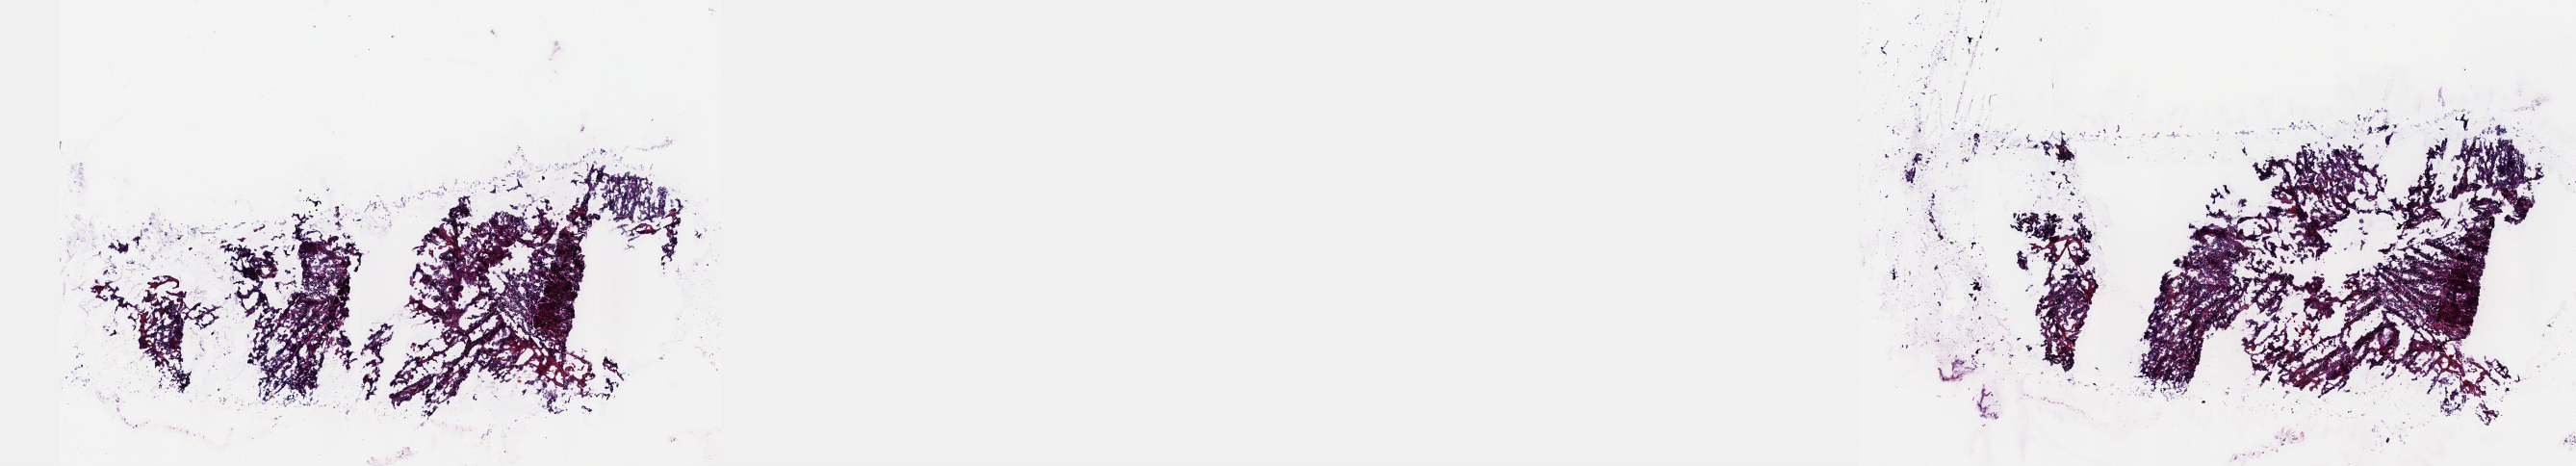
Whole-slide histology image, H&E-stained — a low-resolution overview of the entire scanned area, about 21.6 x 3.9 mm, formalin-fixed paraffin-embedded (FFPE) diagnostic section, primary tumour sample from the cervix. Female, age 43 years at initial diagnosis. Histologic grade: G3 (poorly differentiated). Slide review estimates, as recorded: tumour cells 80%, tumour nuclei 80%, normal cells 0%, stromal cells 20%, necrosis 0%. Infiltration values recorded for this section: lymphocyte infiltration 0%, monocyte infiltration 0%, neutrophil infiltration 0%.
Pathologic diagnosis: Squamous cell carcinoma, large cell, nonkeratinizing, NOS (cervix uteri). FIGO stage: IIB.